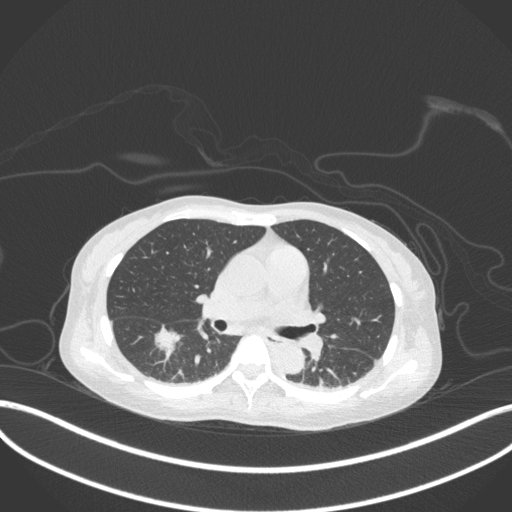
Chest CT, one axial slice; position 173 of 260 along the scan axis; reconstruction kernel B31f; lung window (W 1500 / L -600 HU); 512 × 512 image matrix. Female patient, age 44 years. Case-level facts recorded for this patient, not image findings: clinical TNM (as recorded): T1c N0 M0.
Structures marked on this image (rectangle marked by the reading radiologist):
- lung tumour (recorded histology: adenocarcinoma): box from (x=153, y=325) to (x=182, y=361) px